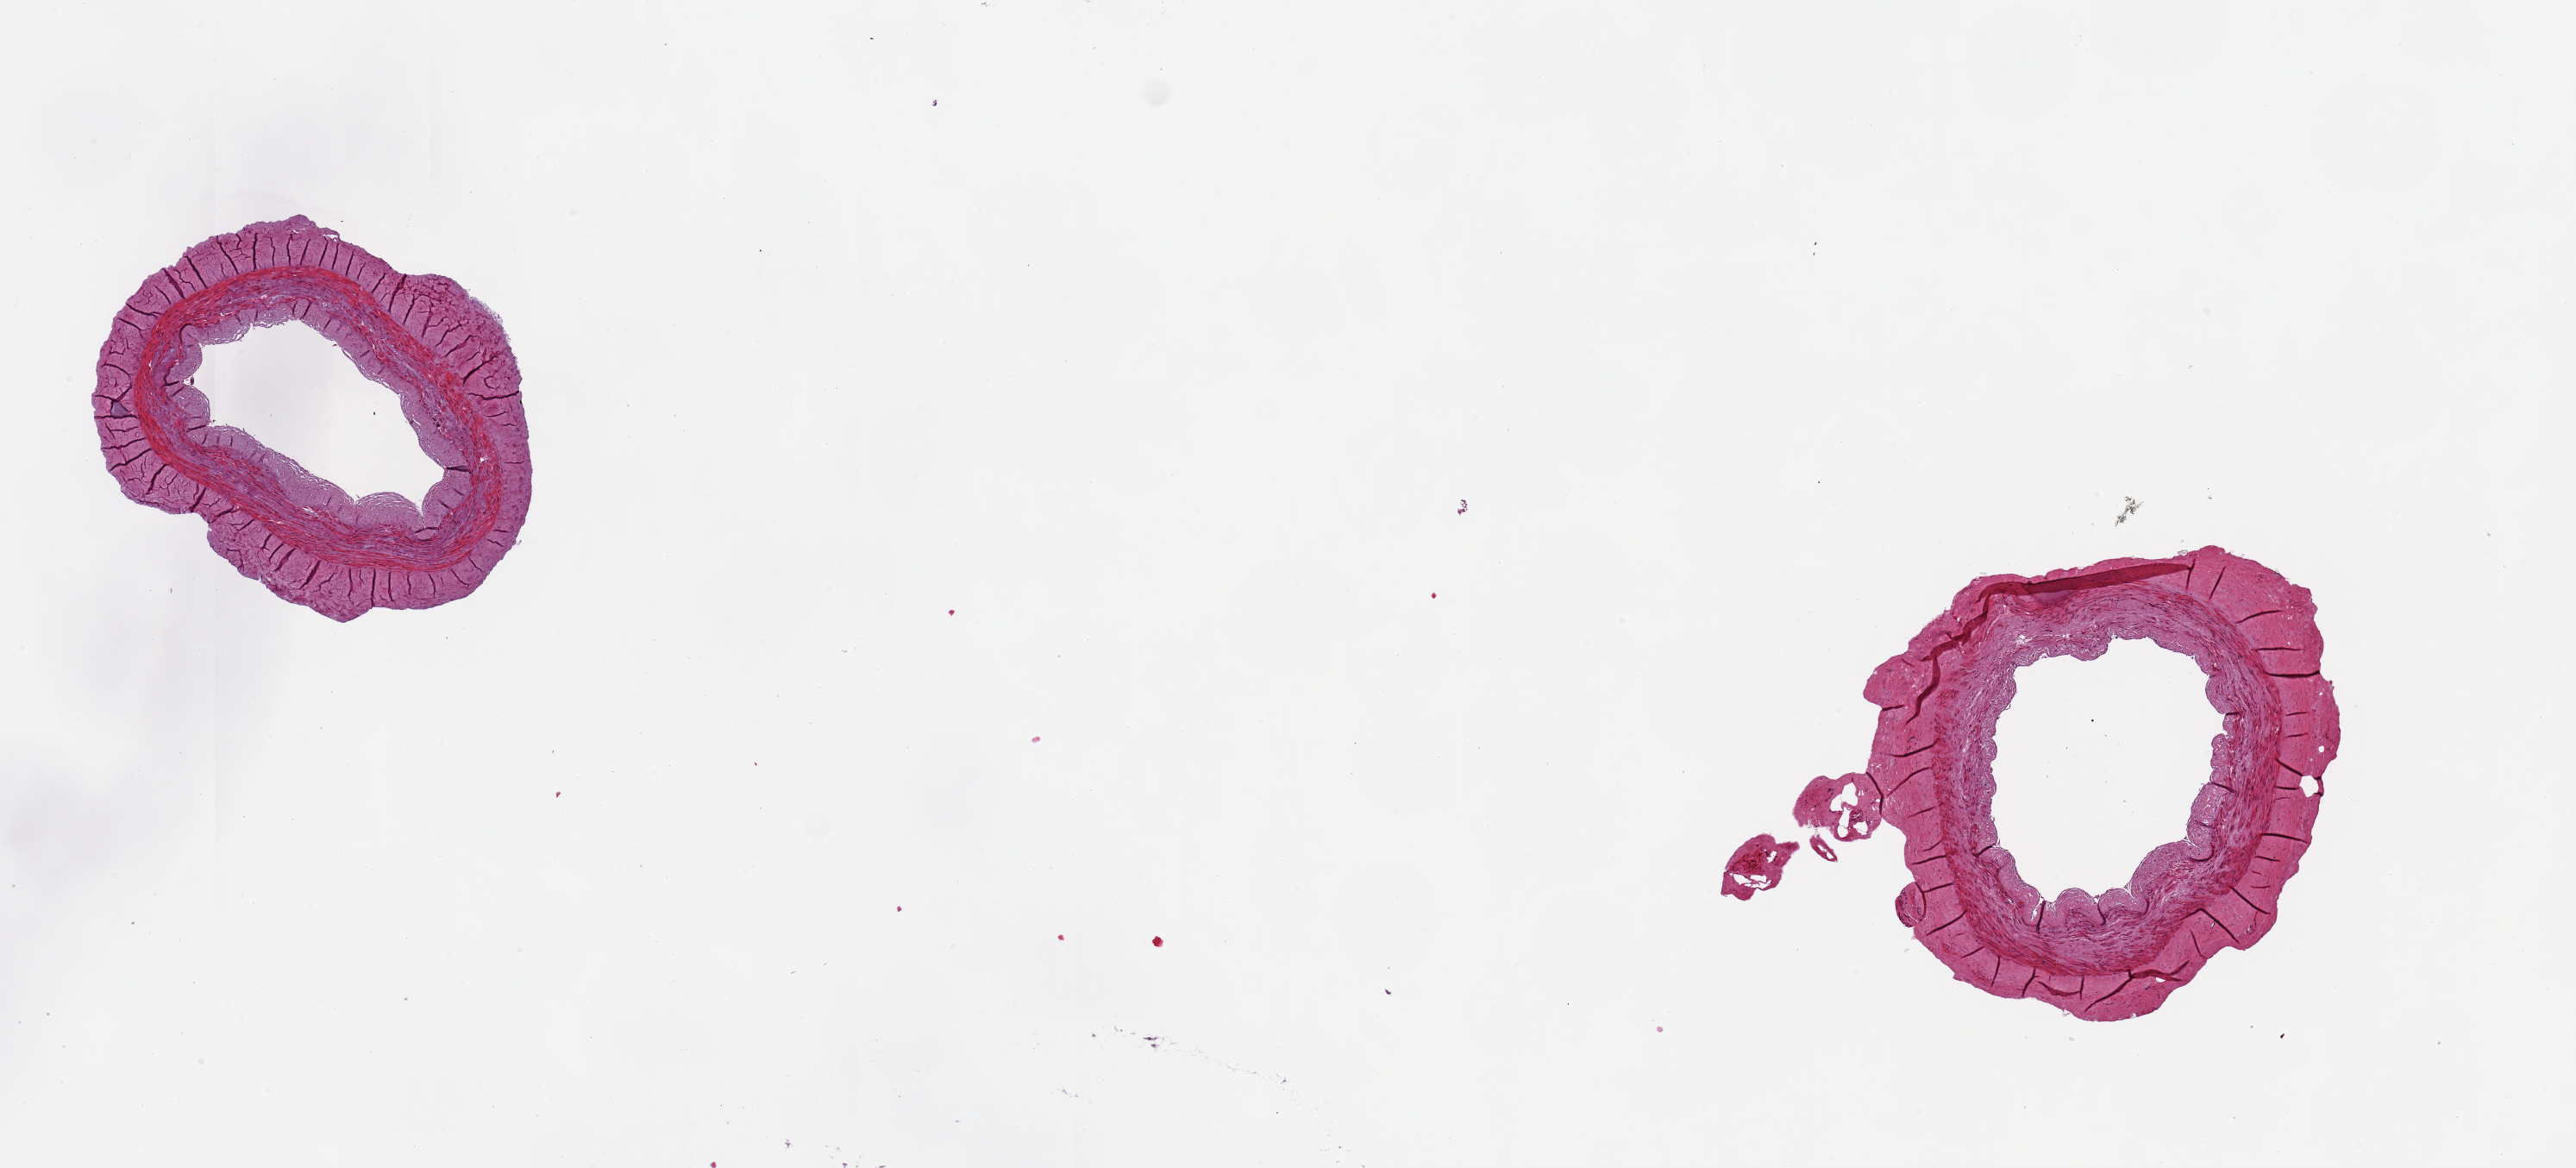
Whole-slide image, hematoxylin and eosin (H&E) stain, low-resolution overview of the scanned area, about 11.8 x 5.4 mm. PAXgene-fixed paraffin-embedded (PFPE) section. Target tissue: tibial artery. Tissue donor sample. Donor sex: female.
• review note (as recorded): 2 pieces, 2x2 & 3x2mm; good clean specimens; no adherent fat